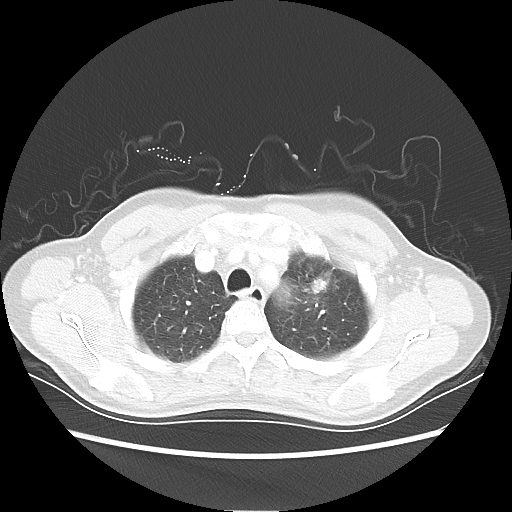
Chest CT, one axial slice; slice 44 of 54 in the series (ordered by position); lung window (W 1500 / L -600 HU); 5 mm slice thickness; 512 × 512 image matrix, field of view 360 × 360 mm. Female patient, age 53 years. Case-level facts recorded for this patient, not image findings: clinical TNM (as recorded): T1c N0 M0.
Annotated regions visible in this slice (bounding box drawn by a radiologist):
- lung tumour (recorded histology: adenocarcinoma): bounding box [x1, y1, x2, y2] px = [306, 275, 336, 295]
- lung tumour (recorded histology: adenocarcinoma): [308, 274, 325, 292]